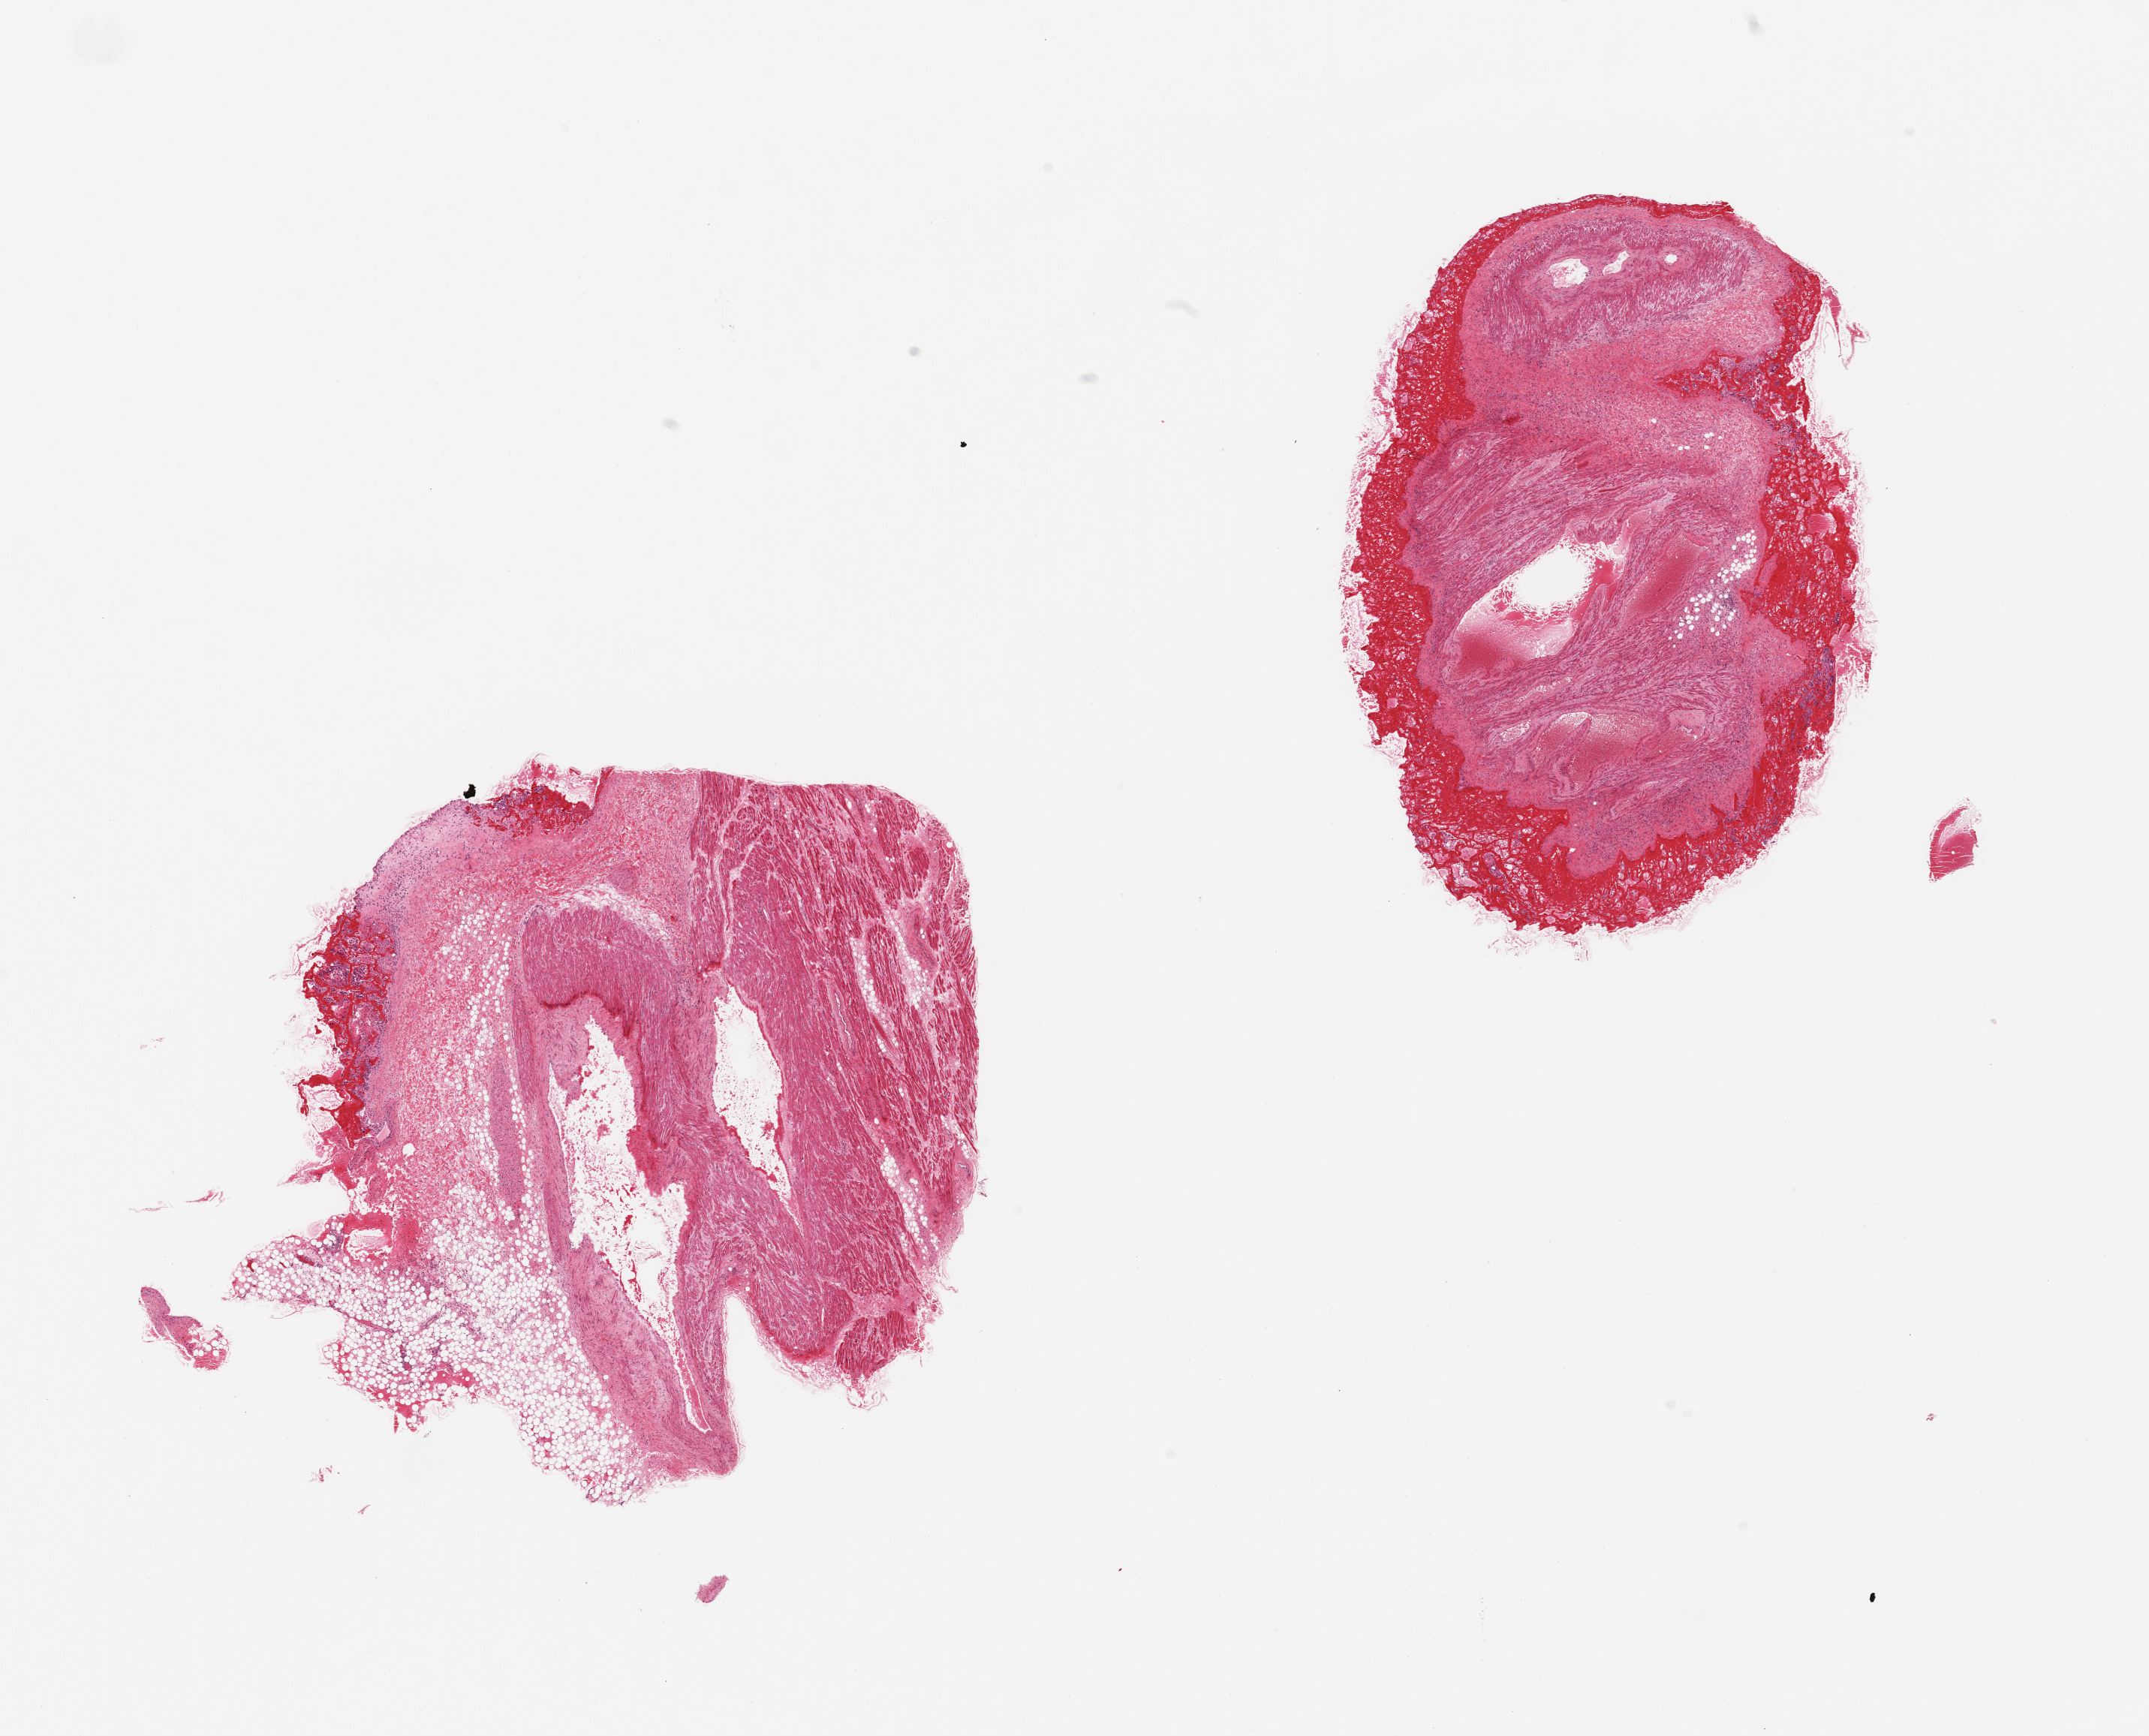
Digitized hematoxylin and eosin (H&E)-stained section, a low-resolution overview of the entire scanned area, about 22.6 x 18.3 mm (slide scanned at 20x), PAXgene-fixed paraffin-embedded (PFPE) section, section of auricular appendage (target tissue), tissue donor sample.
- review note (as recorded): 2 pieces no abnormalities, unusual rim of adherent hmorrhage/clot